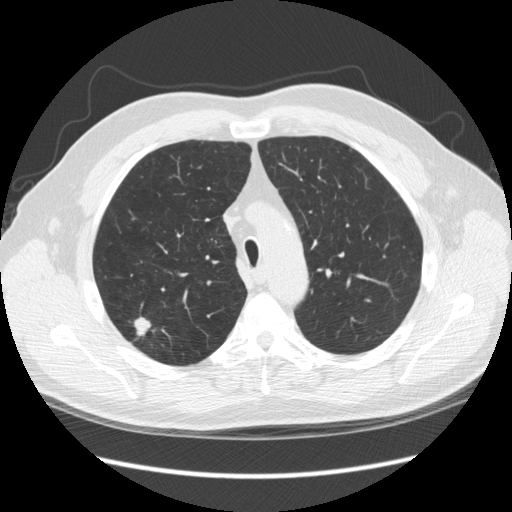
Low-dose screening chest CT, axial slice, third screening round (two years after baseline), lung window (W 1500 / L -600 HU), 2.5 mm slice thickness, 512 × 512 image matrix. Male, age 64 years at enrolment. Former smoker at enrolment.
Expert reader's lesion annotation, box from (x=118, y=313) to (x=170, y=356) px. The screening reader recorded 4 non-calcified nodules or masses ≥4 mm on this exam (right upper lobe, right upper lobe, right upper lobe, right upper lobe); which of them this box marks is not recorded. Official screen result: positive, other.